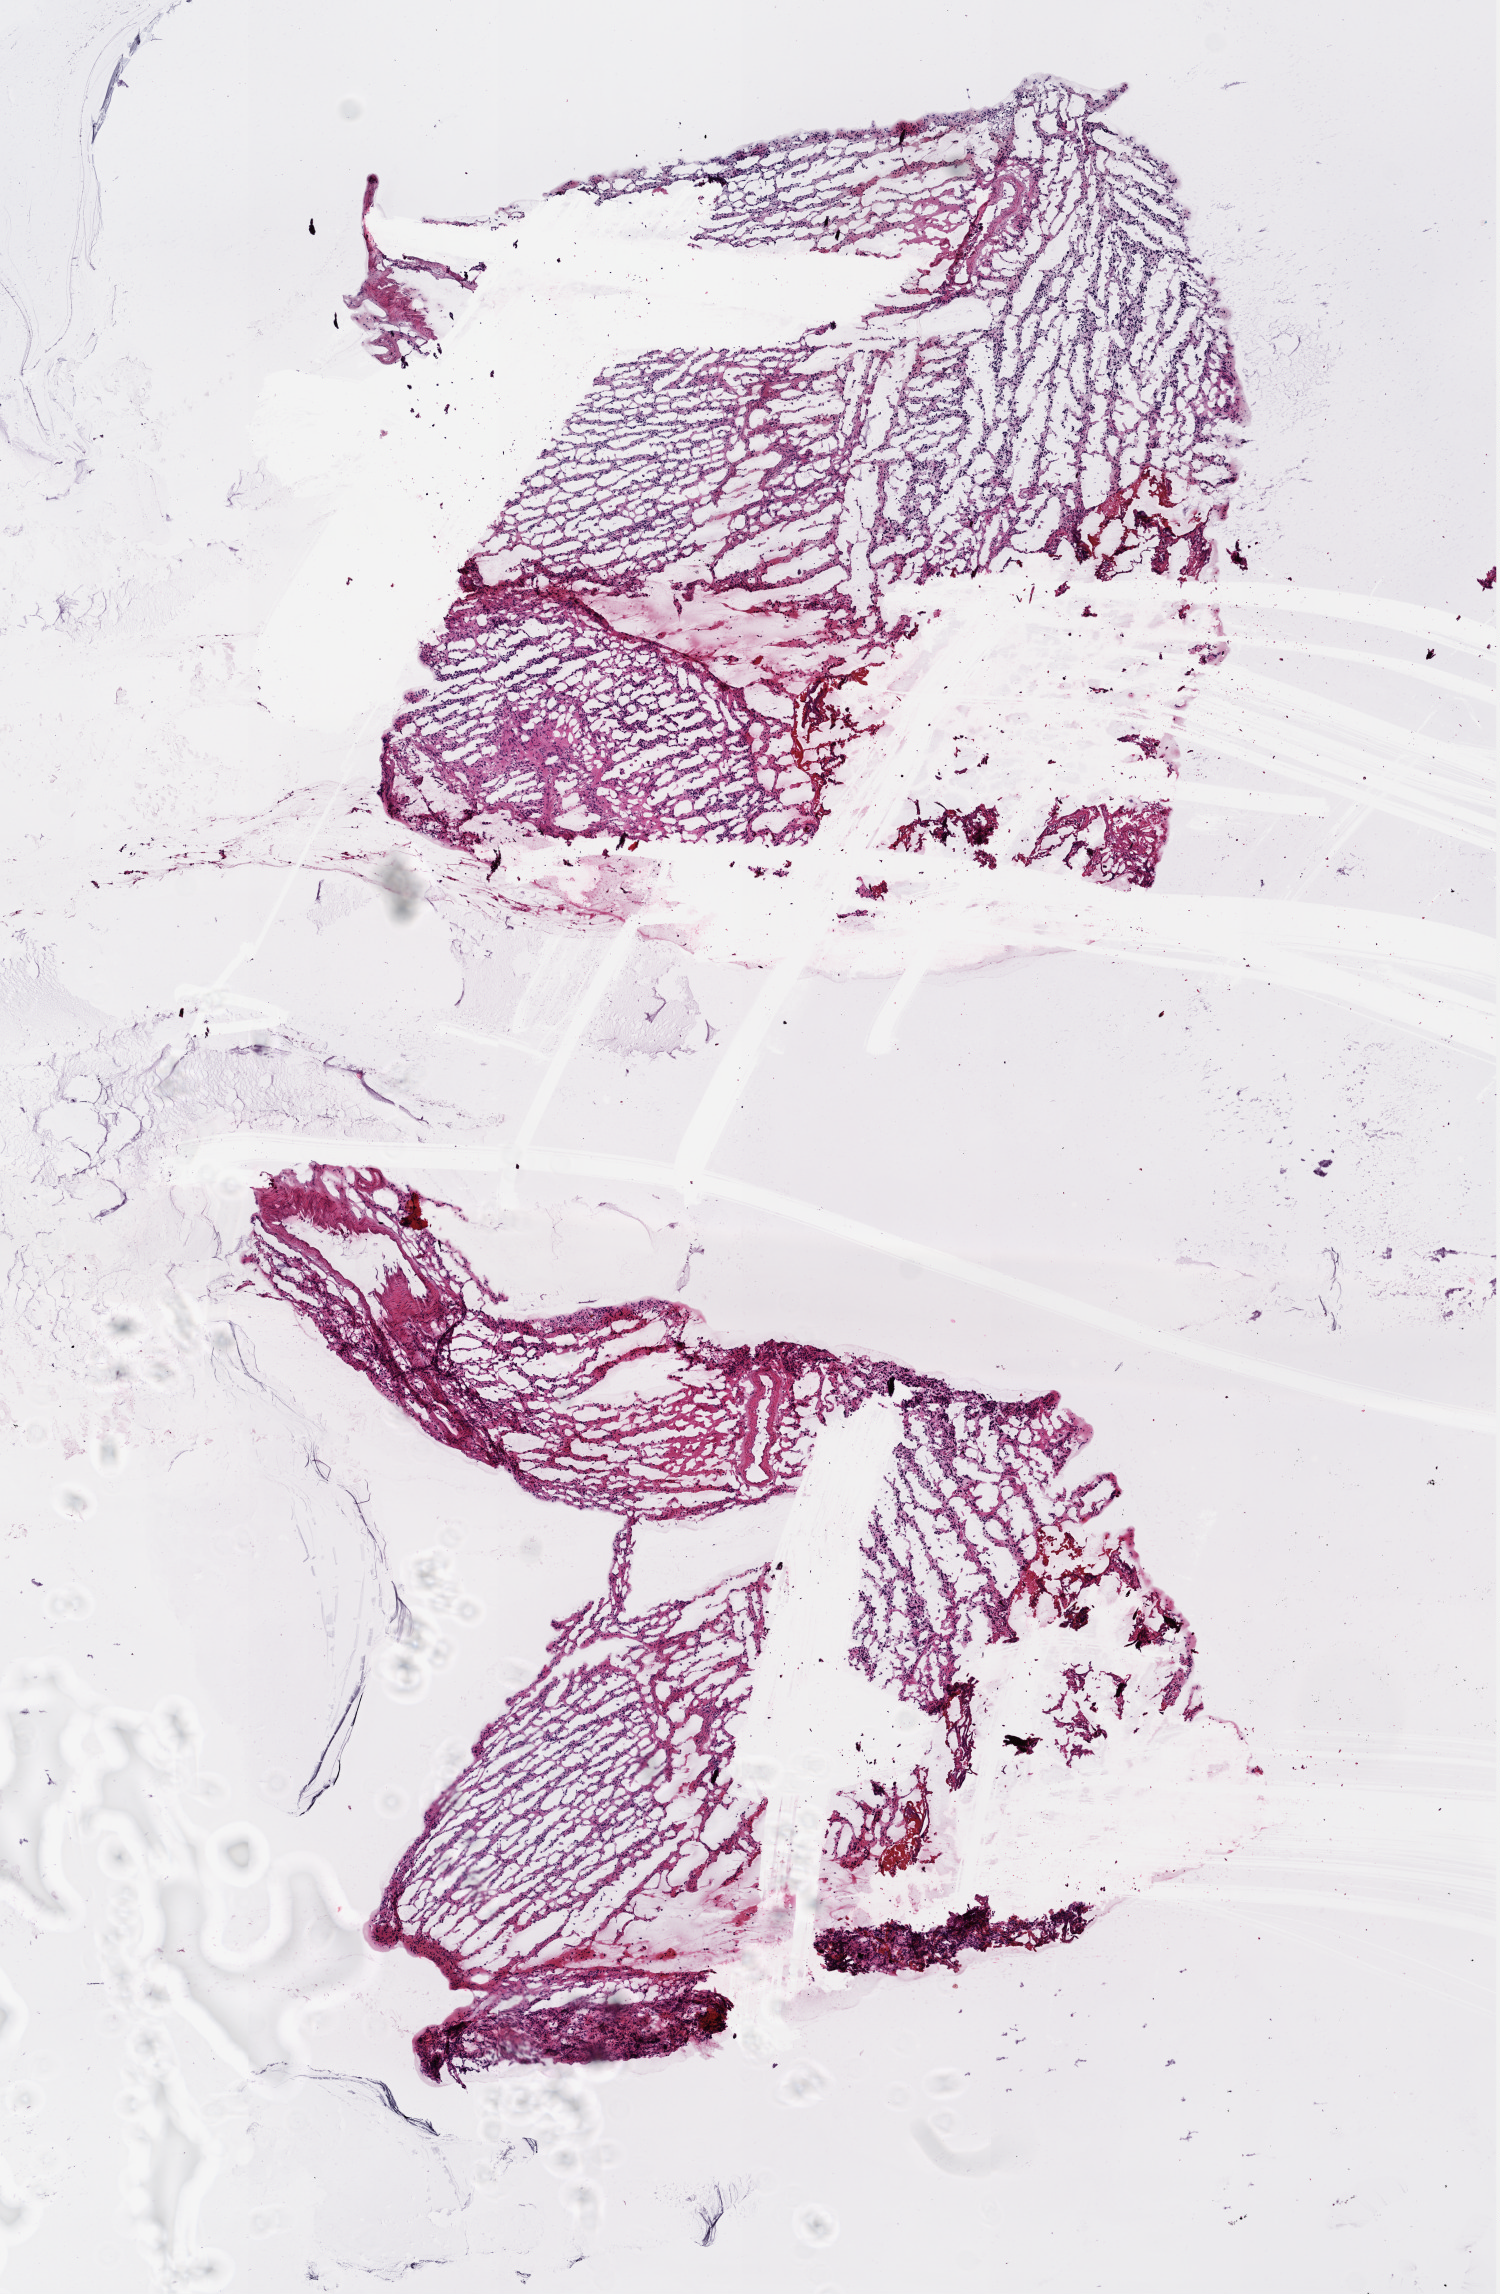
Hematoxylin and eosin (H&E) stained whole-slide image — low-resolution overview of the scanned area, about 6.0 x 9.2 mm (acquisition: 20x scan). Frozen section from the top of the tissue portion. Primary tumour sample from the brain. Female patient; age at initial diagnosis 38 years.
Diagnosis: Mixed glioma.